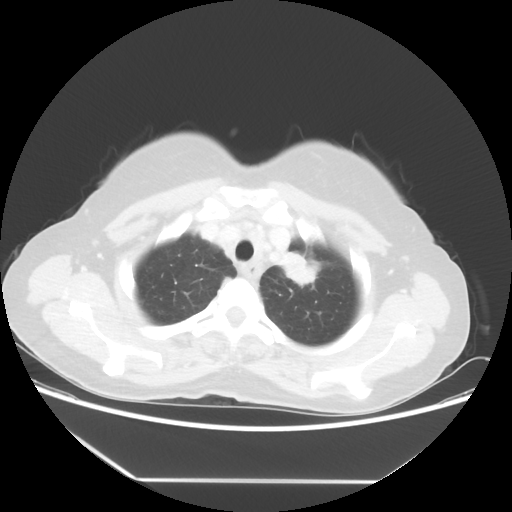
Chest CT, one axial slice. Position 45 of 52 along the scan axis. Reconstruction kernel STANDARD. Lung window (W 1500 / L -600 HU). 5 mm slice thickness. 512 × 512 image matrix, field of view 390 × 390 mm. Female patient, age 50 years. Case-level facts recorded for this patient, not image findings: clinical TNM (as recorded): T2 N3 M0.
Annotated regions visible in this slice (rectangle marked by the reading radiologist):
- lung tumour (recorded histology: adenocarcinoma): bounding box (x1, y1, x2, y2) in pixels: (278, 238, 322, 287)